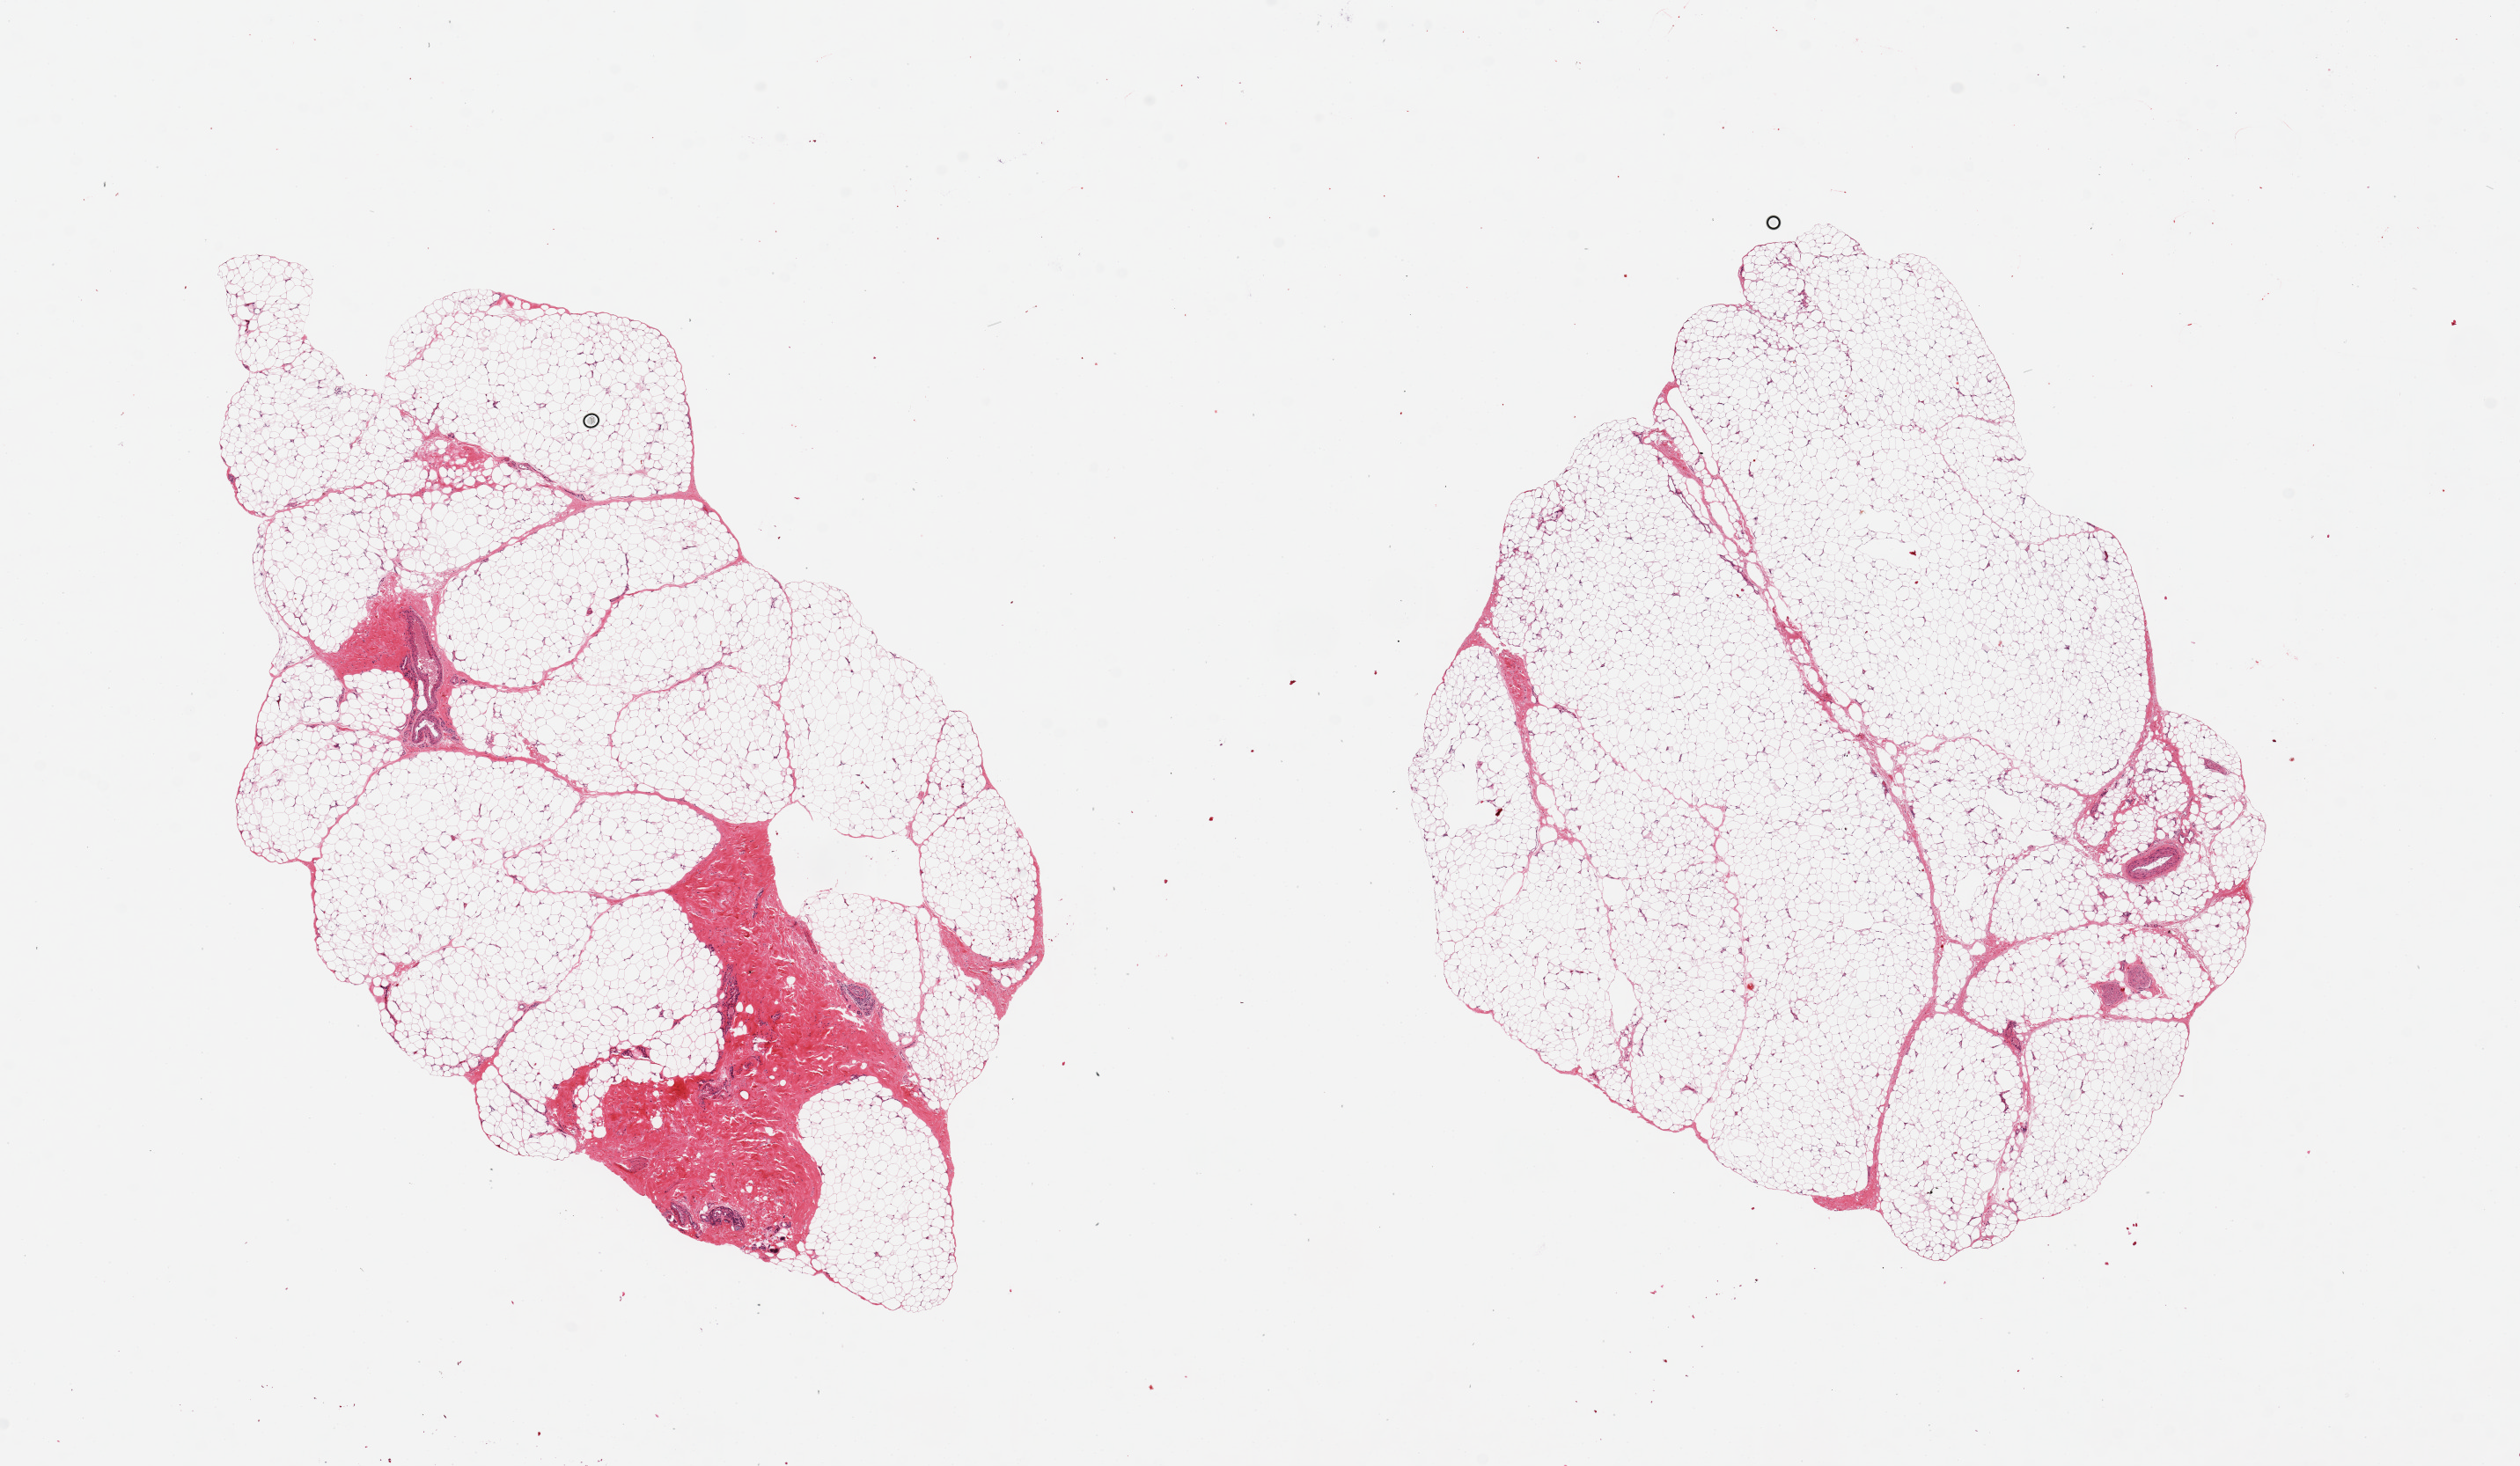
Digitized hematoxylin and eosin (H&E)-stained section — a low-resolution overview of the entire scanned area, about 22.6 x 13.2 mm, PAXgene-fixed paraffin-embedded (PFPE) section, target tissue: adipose tissue, tissue donor sample. Male donor.
• reviewer comment on this tissue sample: 2 pieces ~9x6mm